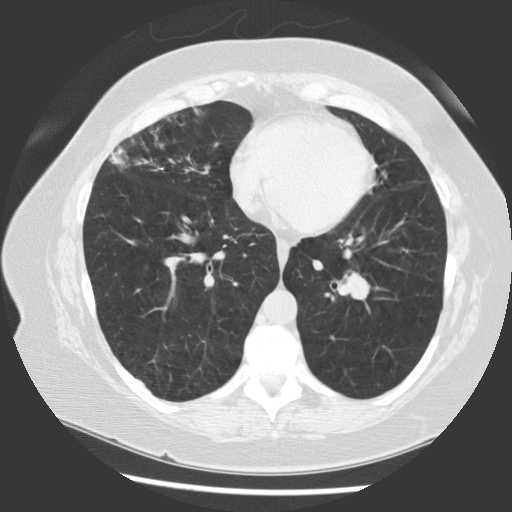
Low-dose screening chest CT, one axial slice. Slice 54 of 130 in the series (ordered by position). Reconstruction kernel STANDARD. 120 kVp. Lung window (W 1500 / L -600 HU). 2.5 mm slice thickness. 512 × 512 image matrix.
Outlined on this slice (outlined manually by an expert reader):
- lesion 1 (tumor, hilum of left lung): box from (x=344, y=274) to (x=370, y=300) px